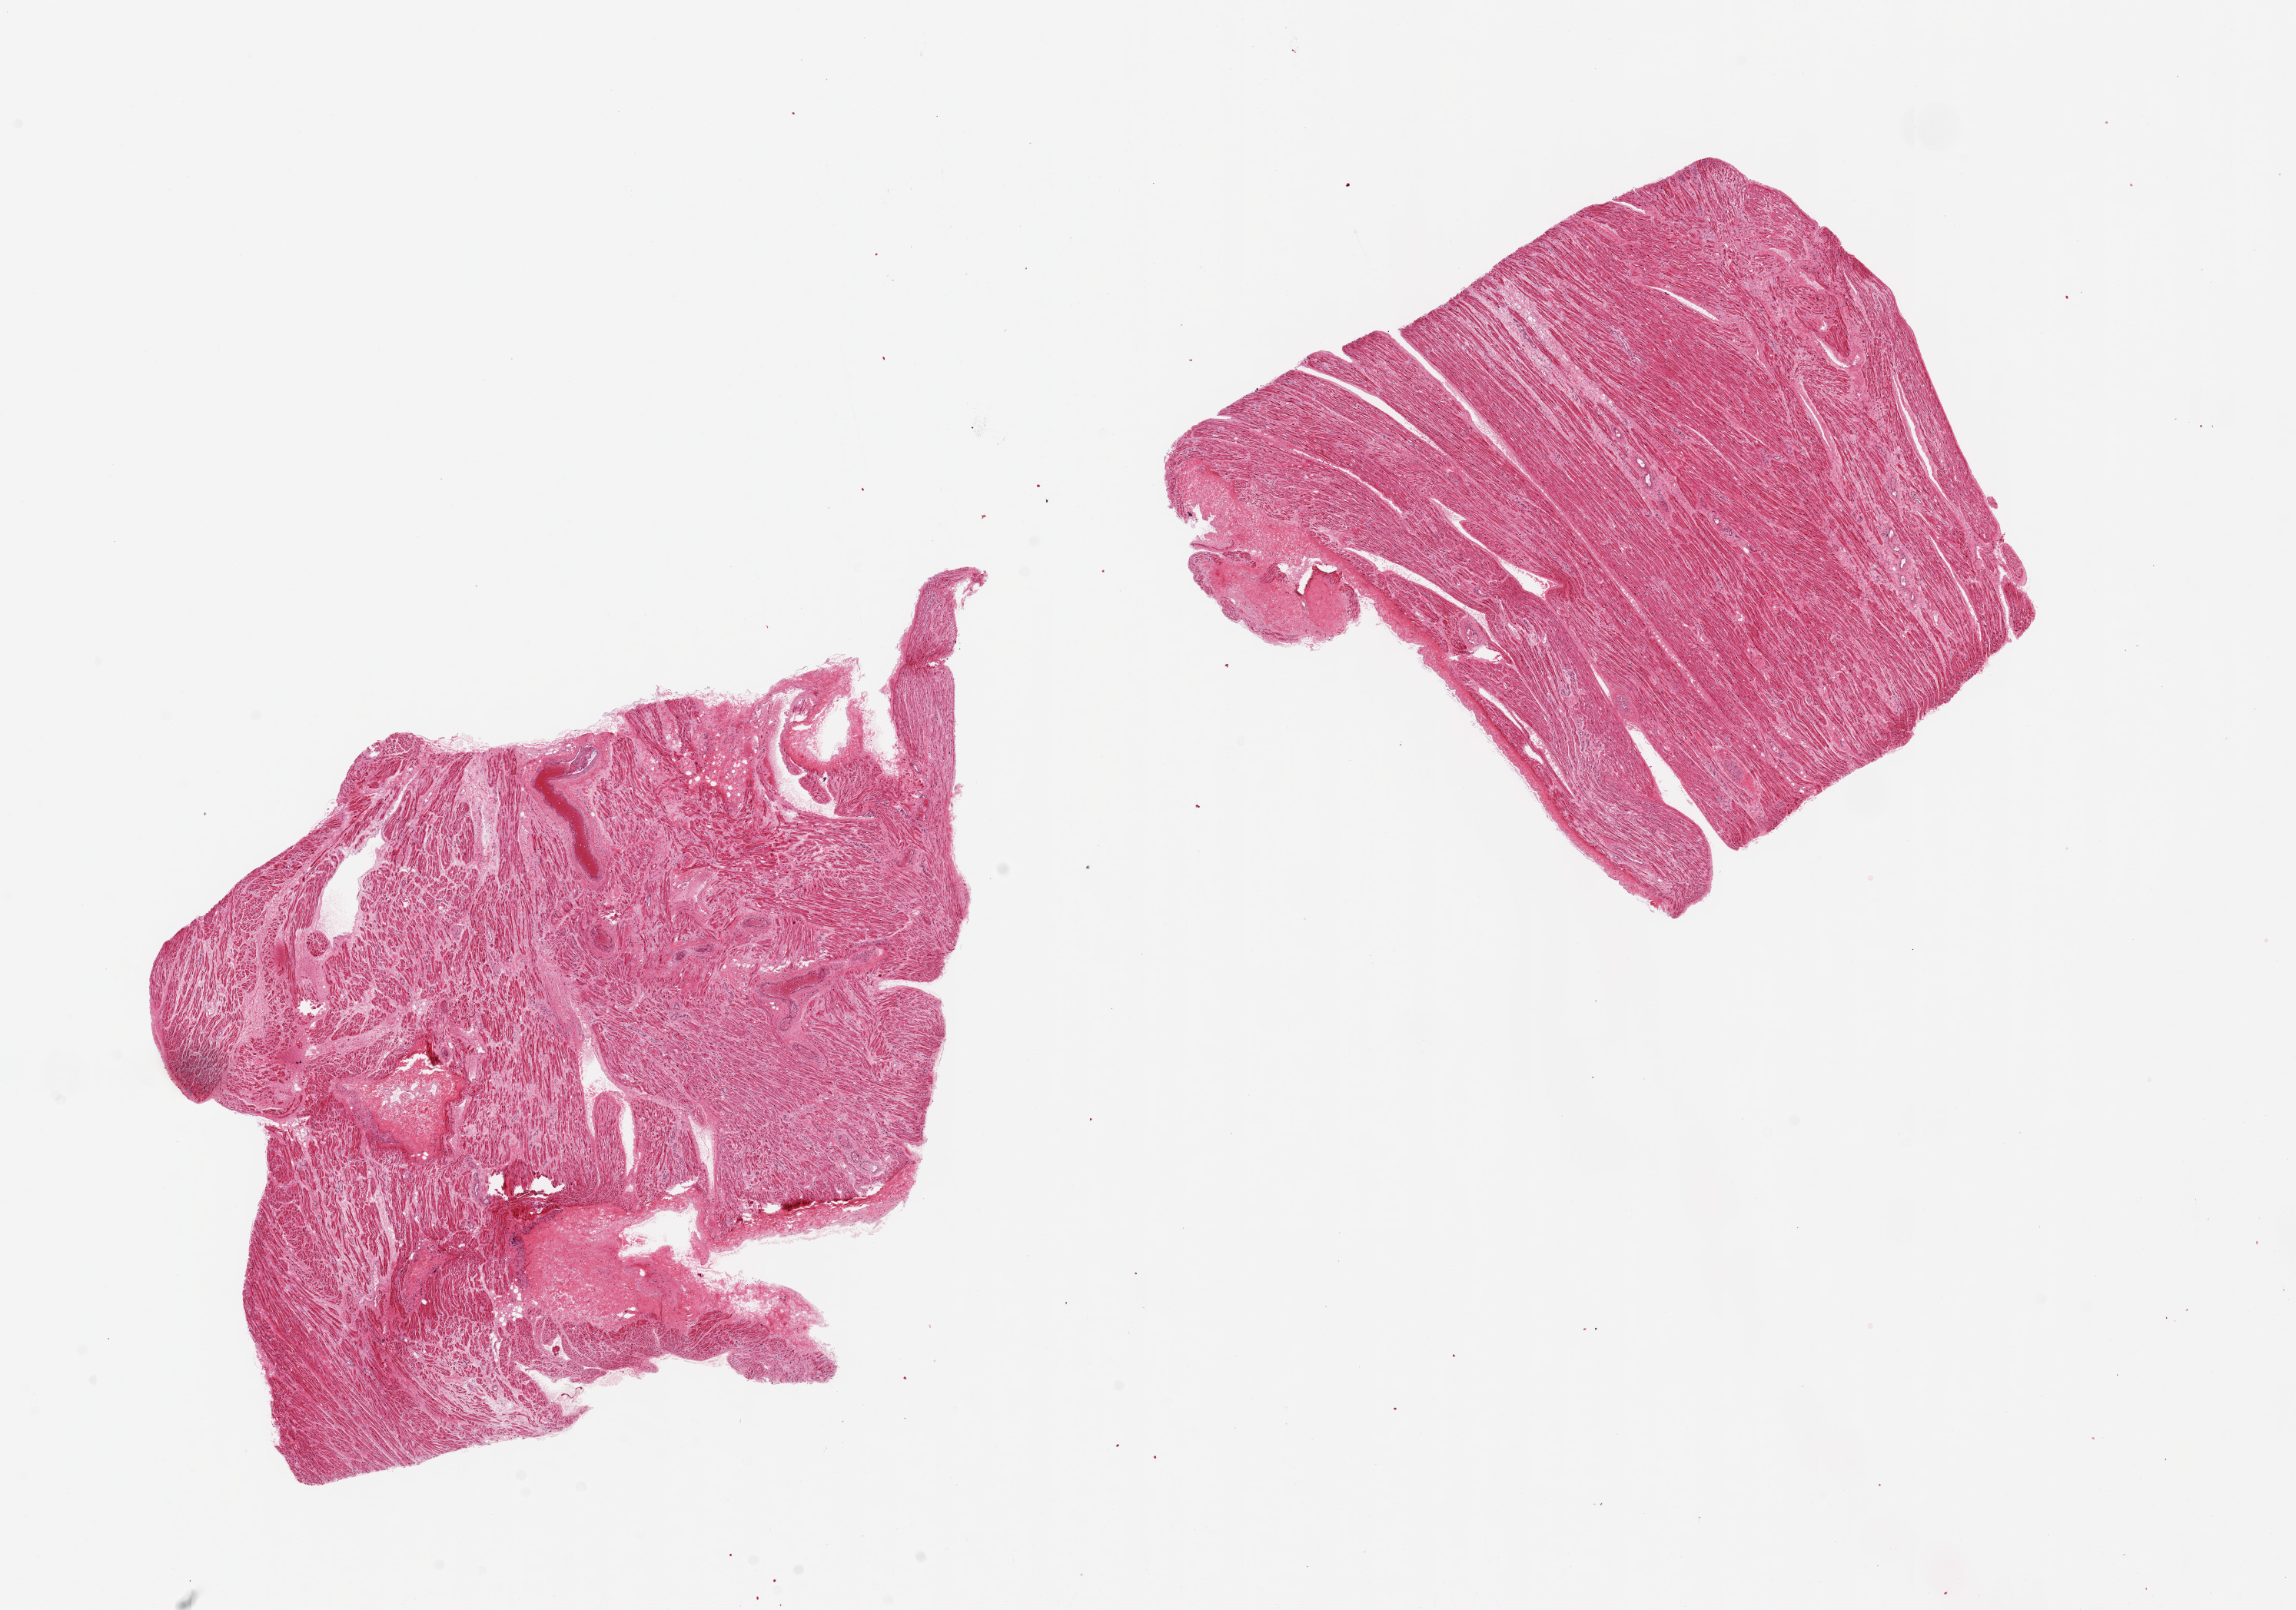
Digitized H&E-stained section, shown as a low-resolution overview of the whole scanned area (about 23.6 x 16.6 mm). PAXgene-fixed, paraffin-embedded tissue. Section of auricular appendage (target tissue). Donor tissue sample. Donor sex: male.
Reviewer comment on this tissue sample: 2 pieces, 9x8 & 7.5x7mm; Mild interstitial fibrosis.